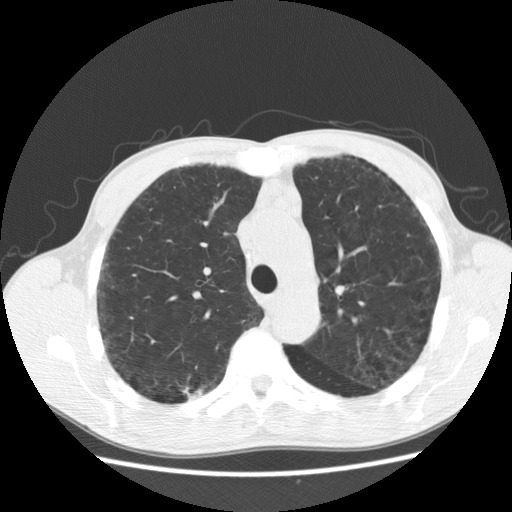
Low-dose screening chest CT, one axial slice. Position 138 of 195 along the scan axis. Reconstruction kernel STANDARD. Lung window (W 1500 / L -600 HU). 512 × 512 image matrix.
Annotated regions visible in this slice (expert manual segmentation):
- lesion 1 (tumor, upper lobe of right lung): bounding box (x1, y1, x2, y2) in pixels: (183, 387, 203, 398)